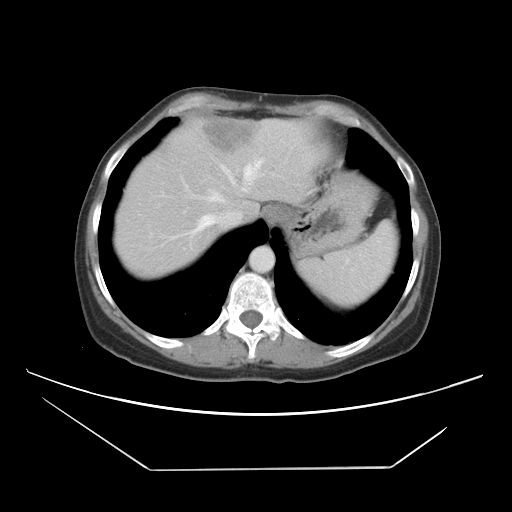
Contrast-enhanced abdominal CT, one axial slice; 120 kVp; intravenous contrast given; soft-tissue window (W 400 / L 40 HU); 5 mm slice thickness; 512 × 512 image matrix, field of view 399 × 399 mm. Female patient, age 52 years. Case-level facts recorded for this patient, not image findings: diagnosis: colorectal cancer liver metastases, imaged before liver resection; multiple liver metastases: yes; largest metastasis: 5.5 cm; chemotherapy before resection: yes.
Outlined on this slice (outlined manually by an expert reader):
- hepatic veins: bounding box <192,159,263,234> (left, top, right, bottom; pixels)
- liver: <116,119,319,277>
- planned liver remnant (the part of the liver to remain after resection): <128,132,228,223>
- portal vein (with intrahepatic branches): <234,145,295,187>
- liver metastasis: <201,122,253,152>